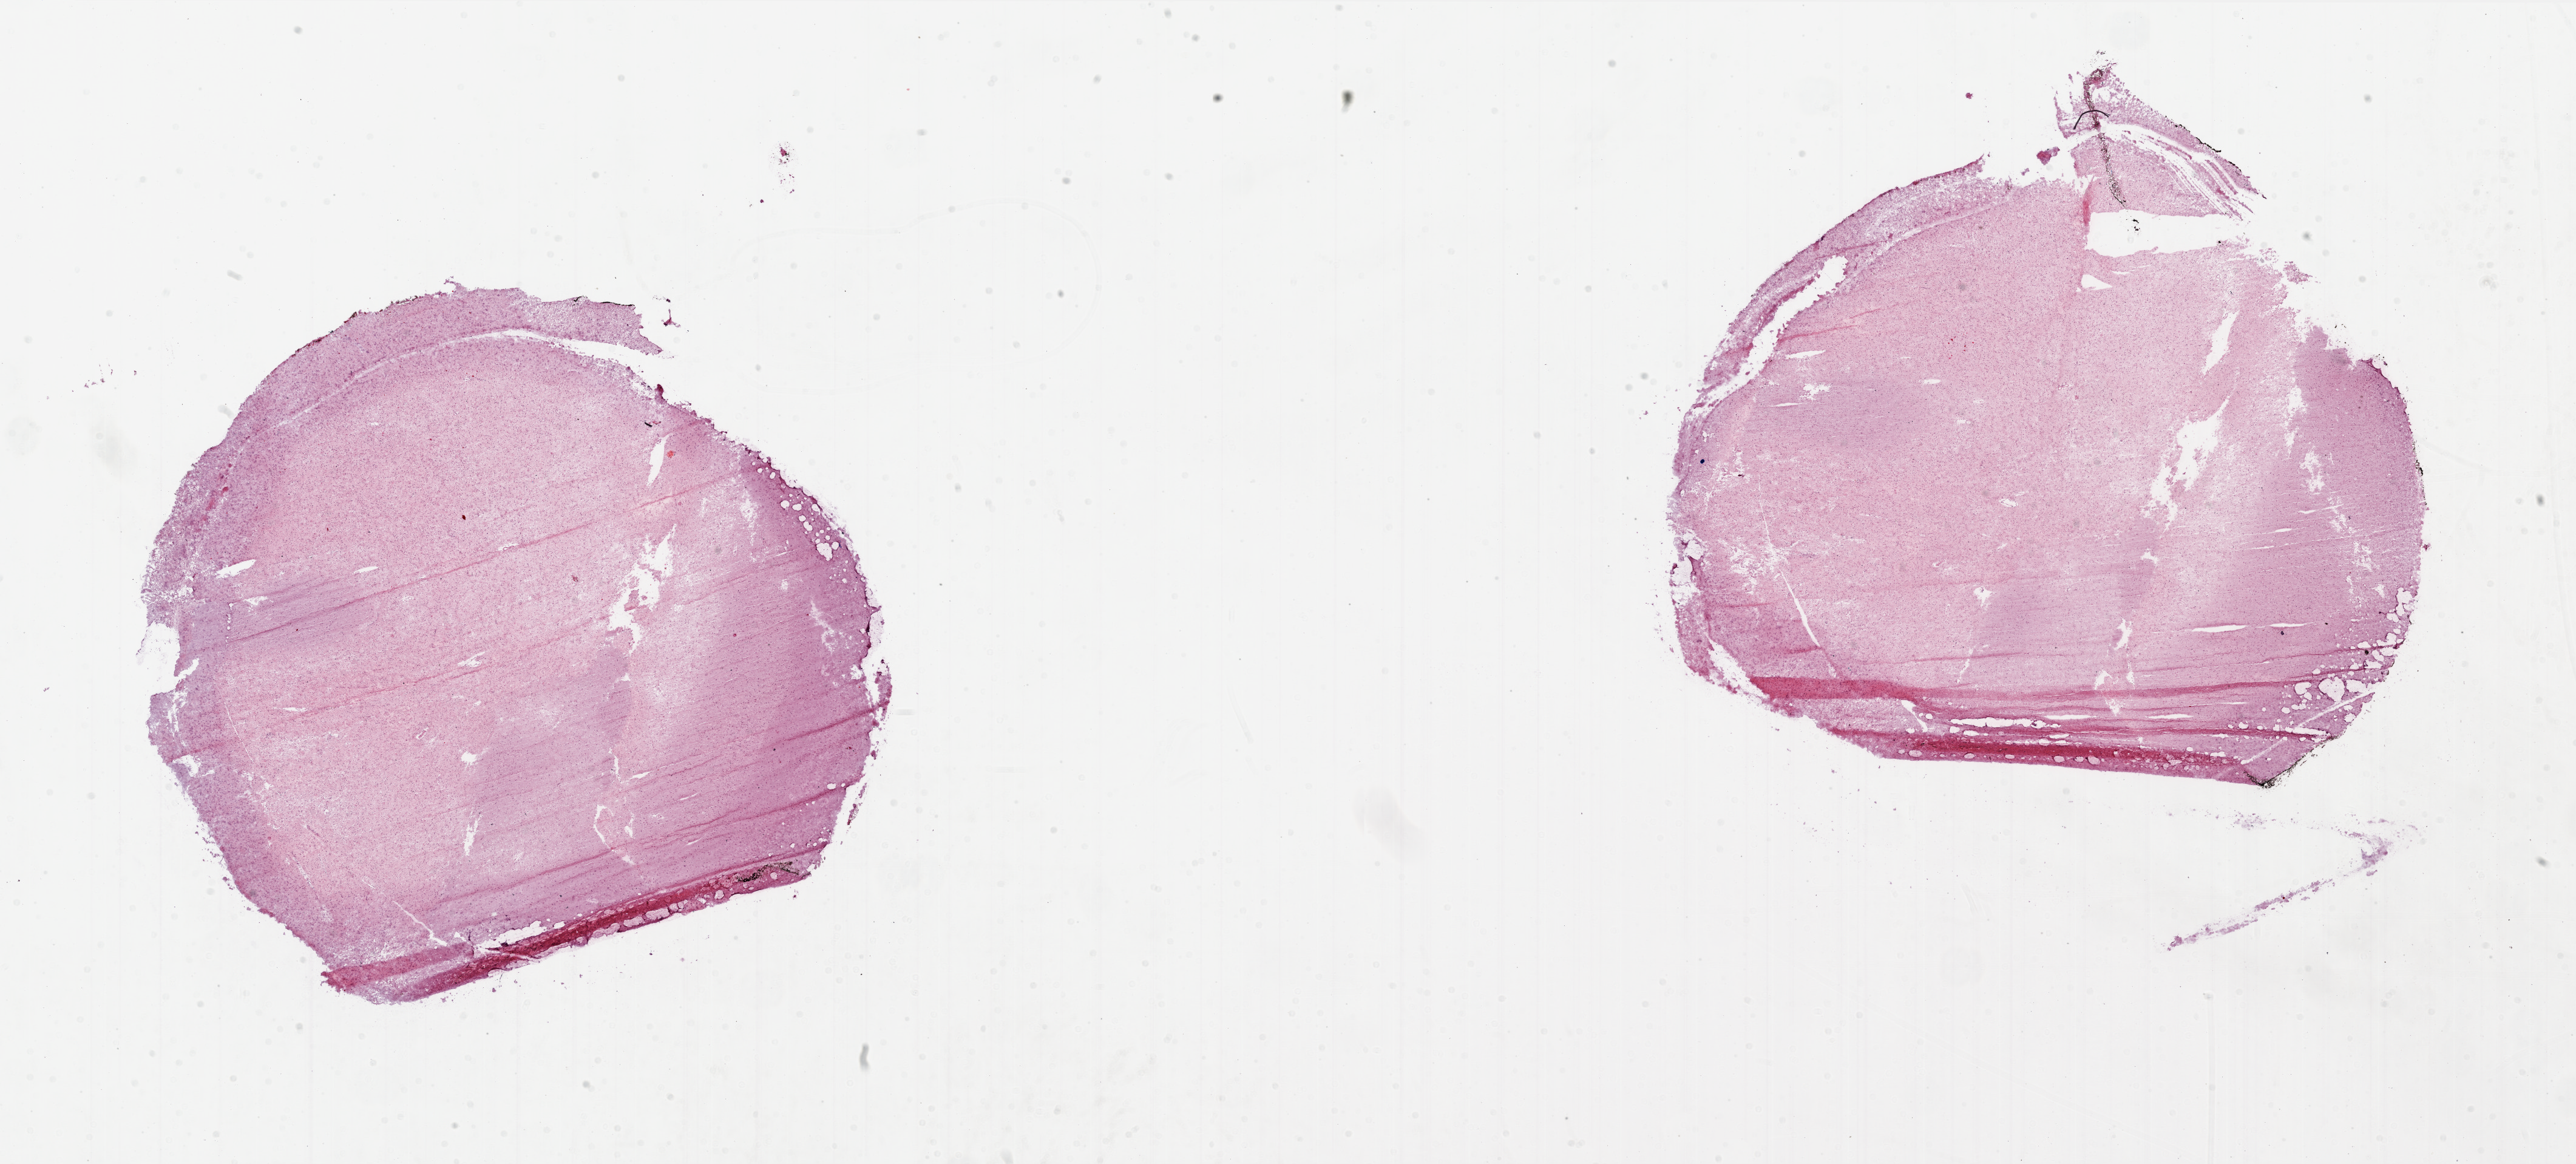
H&E whole-slide image — whole scanned area (about 34.0 x 15.3 mm) shown as a low-resolution overview. Frozen section. Brain, primary tumour sample. Male, age 81 years at initial diagnosis. Slide review estimates, as recorded: tumour cells 0%, tumour nuclei 0%, normal cells 75%, stromal cells 25%, necrosis 0%.
• histologic diagnosis: Glioblastoma